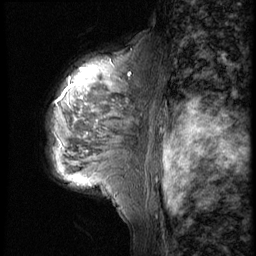
Breast MRI (dynamic contrast-enhanced), one sagittal slice; position 36 of 56 along the scan axis; 4 images stored at this slice position (order not interpretable as contrast timing); 1.5 T; TE 4.2 ms, TR 9 ms; 2.5 mm slice thickness; 256 × 256 image matrix, field of view 180 × 180 mm. Patient: female, 50 years. From the clinical record (not read from this slice): setting: breast cancer imaged before/during neoadjuvant chemotherapy; receptor status: triple-negative.
Structures marked on this image (semi-automatic segmentation, software-assisted and operator-edited):
- analysis volume of interest (the breast-tissue region the enhancement analysis was run in; not a lesion): box from (x=45, y=46) to (x=148, y=188) px
- tumour enhancement mask (voxels above the 140 % enhancement threshold inside the analysis volume of interest): (x=115, y=74)–(x=130, y=80)